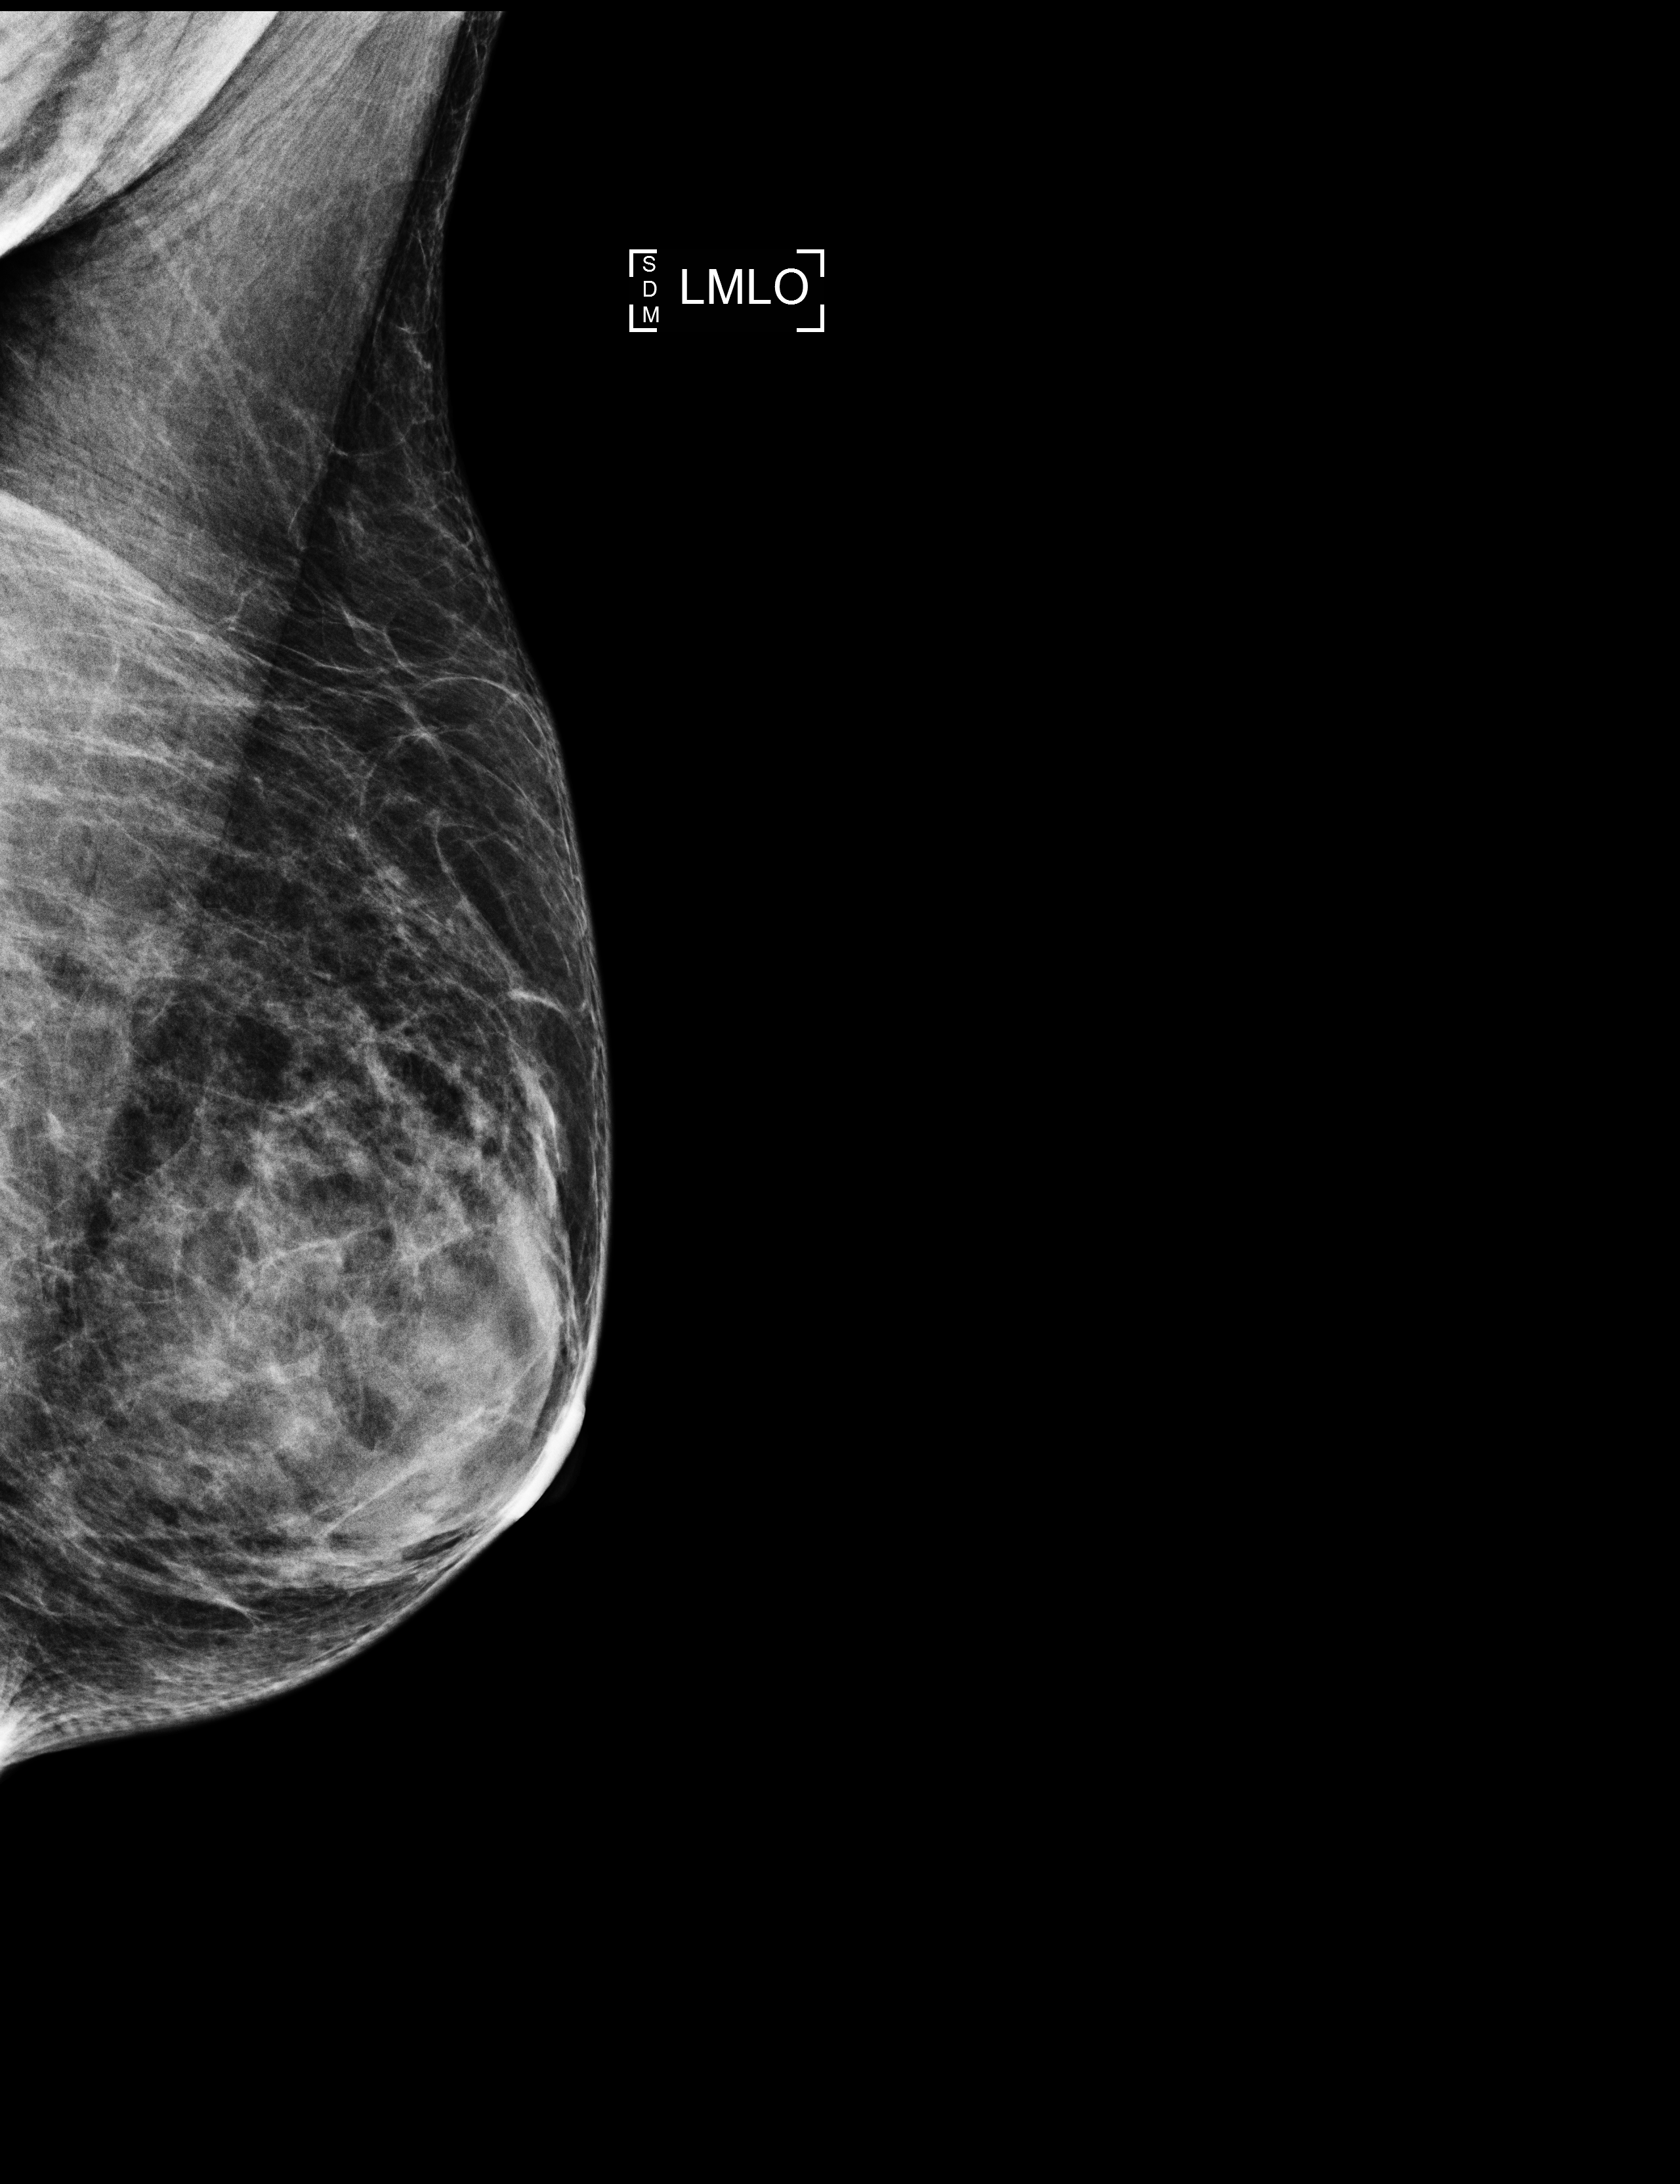
Digital mammogram (FFDM), left breast, medio-lateral oblique projection, screening examination. Patient aged 66 years (female).
- BI-RADS breast density category at the screening exam (both breasts, scale 1–4): 3
- final BI-RADS category for the screening round (tomosynthesis exam, both breasts): category 1
- recall: no recall after this screen